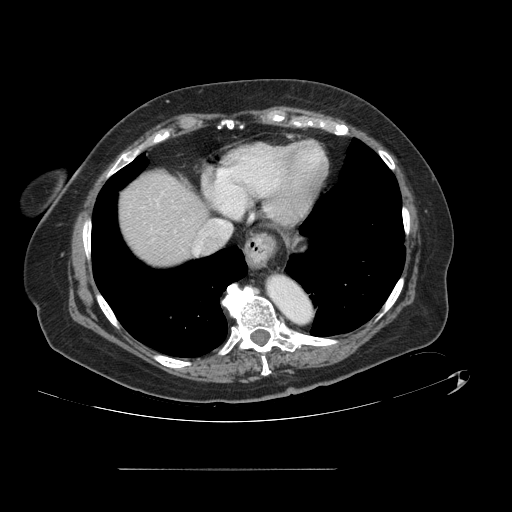
Contrast-enhanced abdominal CT, one axial slice; slice 122 of 148 in the series (ordered by position); 120 kVp; intravenous contrast given; soft-tissue window (W 400 / L 40 HU); 512 × 512 image matrix. Female patient, age 75 years. From the clinical record (not read from this slice): diagnosis: colorectal cancer liver metastases, imaged before liver resection; multiple liver metastases: no; largest metastasis: 2.4 cm; chemotherapy before resection: no.
Structures marked on this image (outlined manually by an expert reader):
- hepatic veins: box from (x=195, y=220) to (x=232, y=253) px
- liver: (x=121, y=173)–(x=206, y=267)
- planned liver remnant (the part of the liver to remain after resection): (x=121, y=172)–(x=206, y=267)